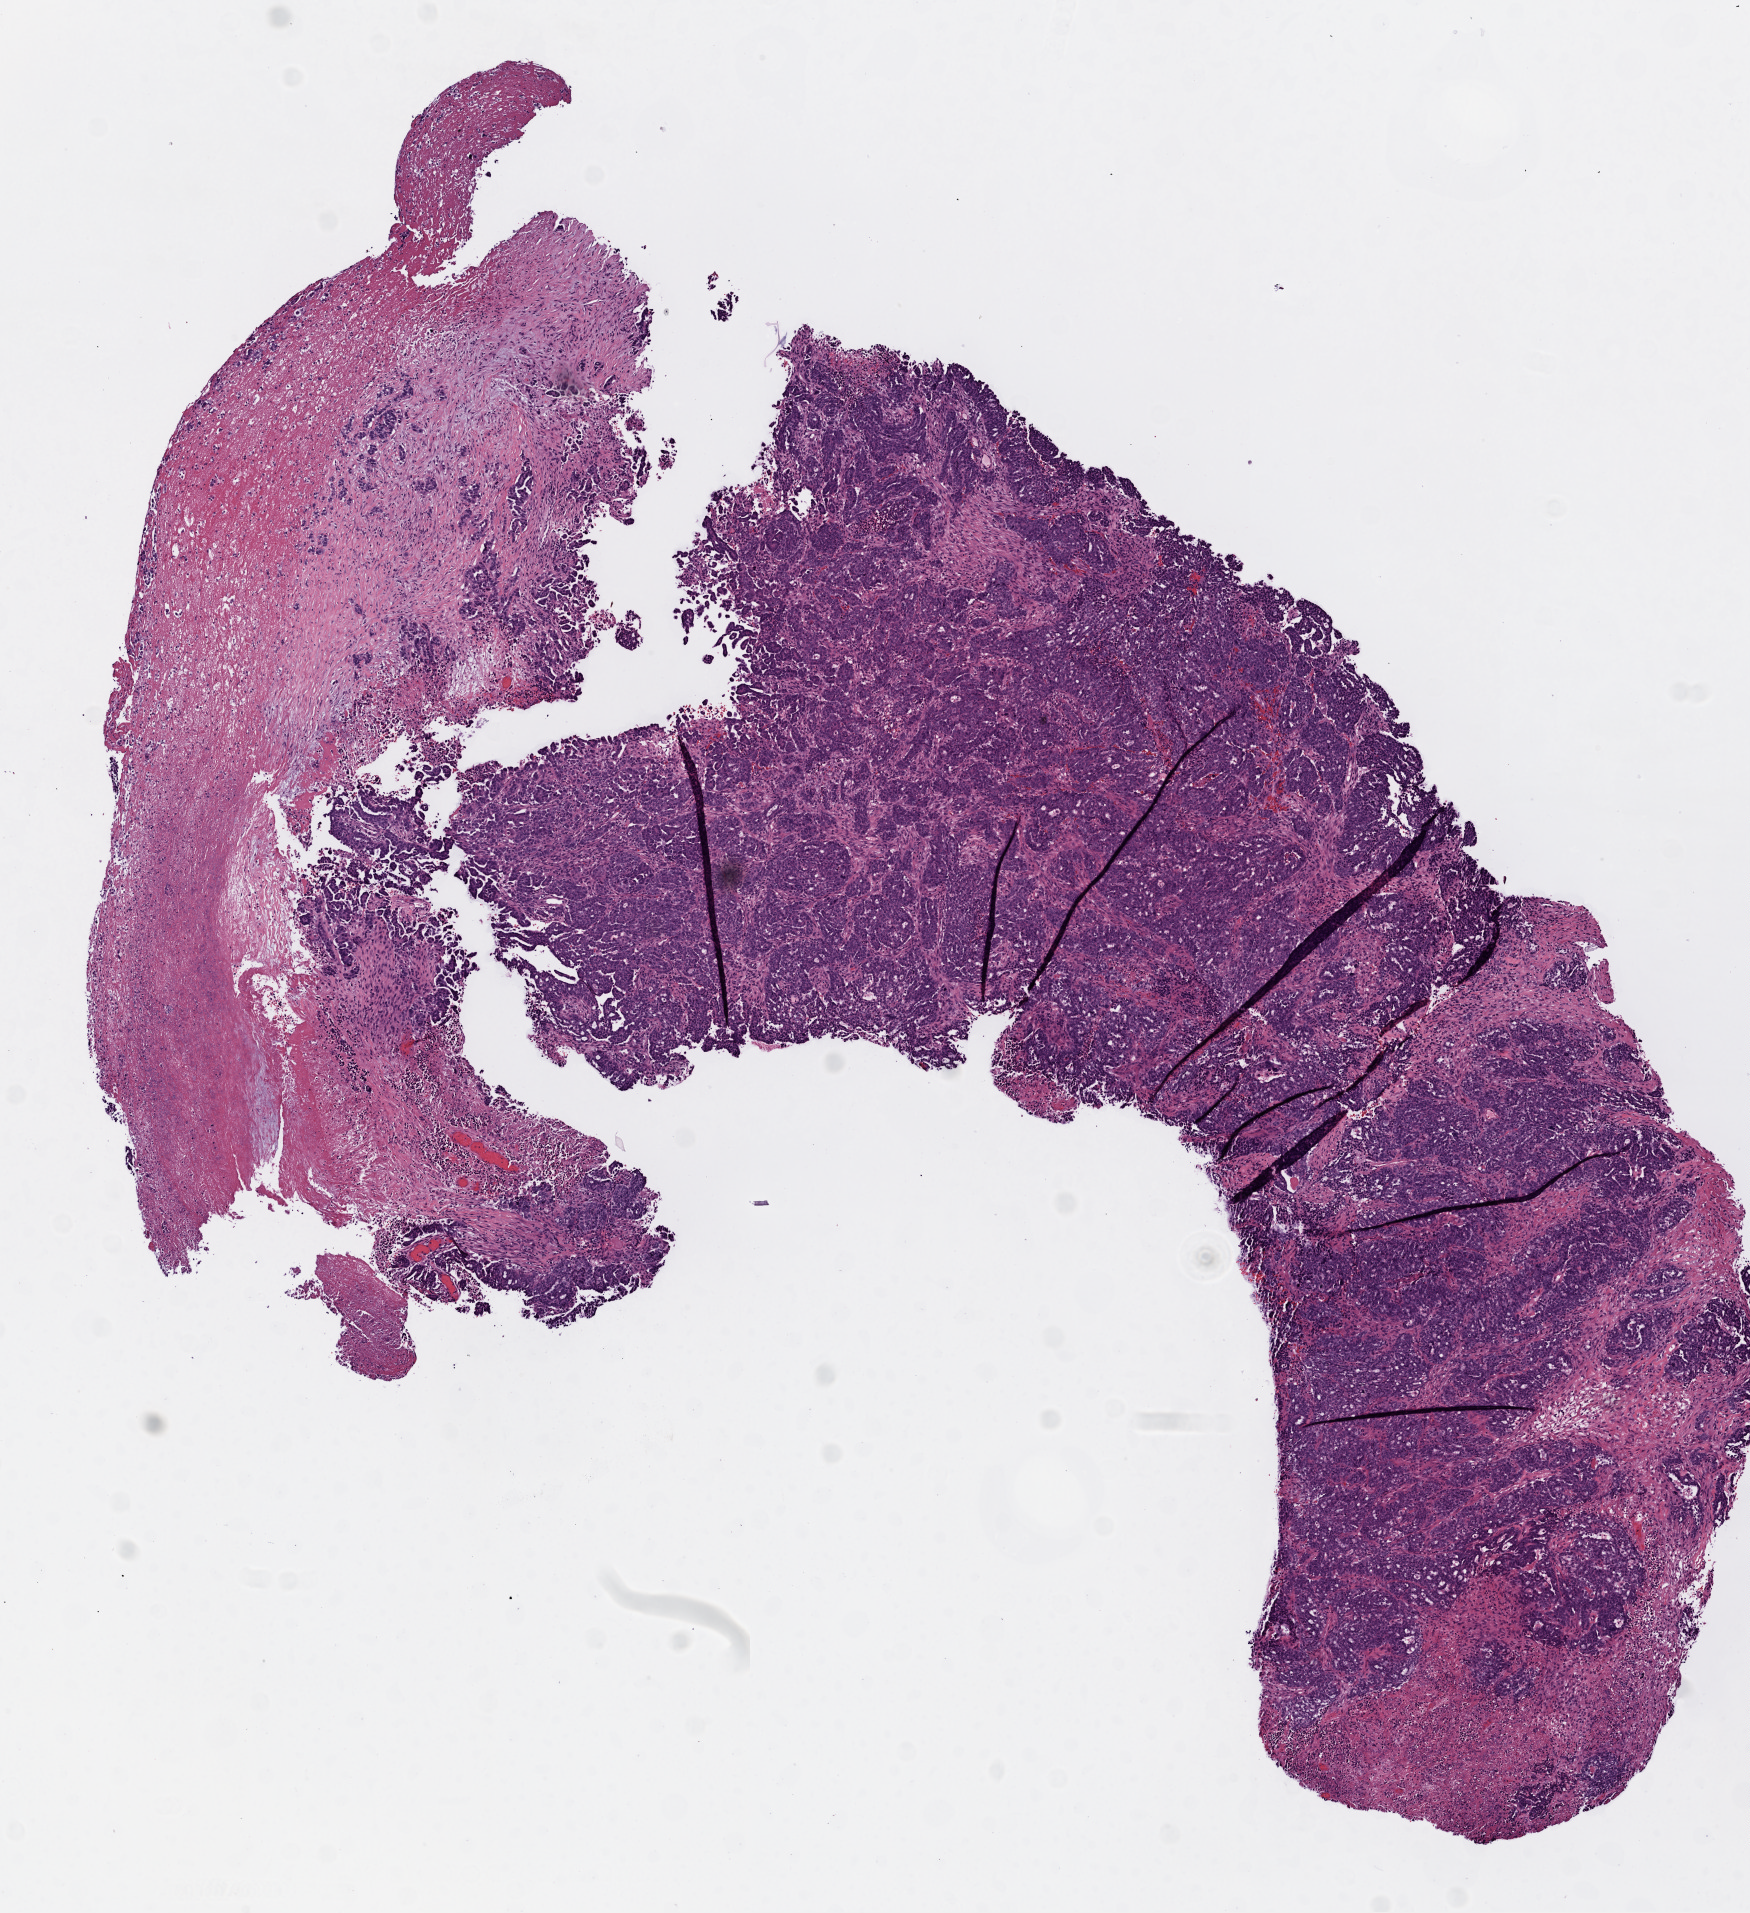
Digitized H&E-stained tissue section (whole slide), low-resolution overview of the scanned area, about 7.0 x 7.7 mm (from a 20x scan); frozen section from the top of the tissue portion; sample: primary tumour, ovary. Female, age 49 years at initial diagnosis. Histologic grade: G3 (poorly differentiated). Pathologist review of this section (percent, as recorded): tumour cells 100%, tumour nuclei 60%, normal cells 0%, stromal cells 0%, necrosis 0%.
Pathologic diagnosis: Serous cystadenocarcinoma, NOS. FIGO stage: IIIC.